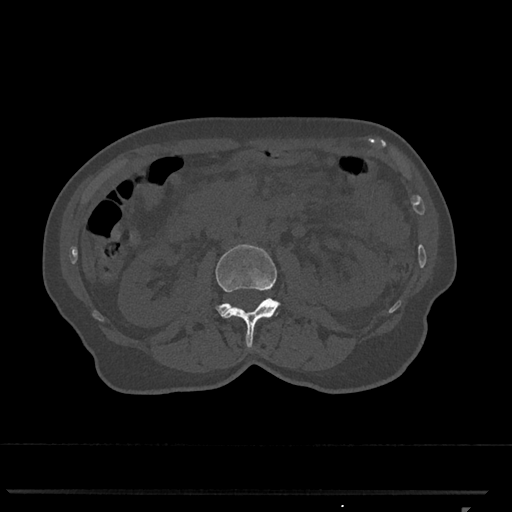
CT including the spine, one axial slice. Position 332 of 793 along the scan axis. 120 kVp. Bone window (W 1800 / L 400 HU). 512 × 512 image matrix. Patient: female, 62 years. Case-level facts recorded for this patient, not image findings: primary cancer: renal.
Structures marked on this image (semi-automatically segmented with operator editing):
- L2 vertebra: bounding box (x1, y1, x2, y2) in pixels: (215, 244, 281, 348)